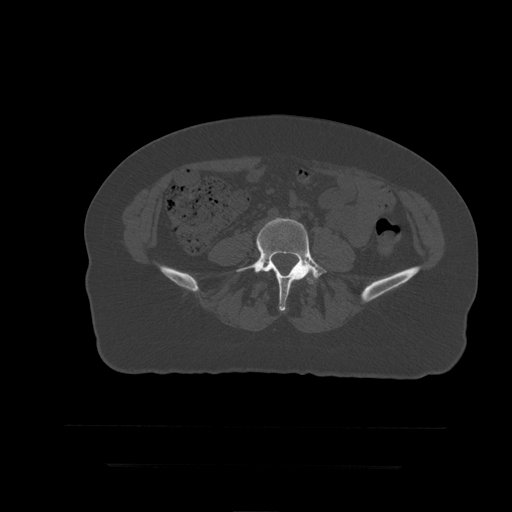
CT including the spine, one axial slice. Slice 77 of 399 in the series (ordered by position). Reconstruction kernel STANDARD. Bone window (W 1800 / L 400 HU). 1.25 mm slice thickness. 512 × 512 image matrix. Patient age 41 years. Case-level facts recorded for this patient, not image findings: primary cancer: breast.
Structures marked on this image (semi-automatic segmentation, software-assisted and operator-edited):
- L5 vertebra: box from (x=236, y=219) to (x=327, y=312) px